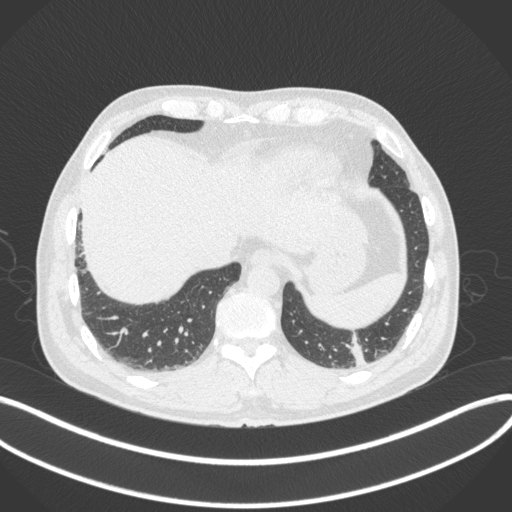
Chest CT, one axial slice; position 52 of 313 along the scan axis; reconstruction kernel B31f; lung window (W 1500 / L -600 HU); 512 × 512 image matrix, field of view 400 × 400 mm. Patient: male, 54 years. Case-level facts recorded for this patient, not image findings: clinical TNM (as recorded): T1c N0 M1.
Outlined on this slice (rectangle marked by the reading radiologist):
- lung tumour (recorded histology: adenocarcinoma): bounding box <344,330,369,366> (left, top, right, bottom; pixels)